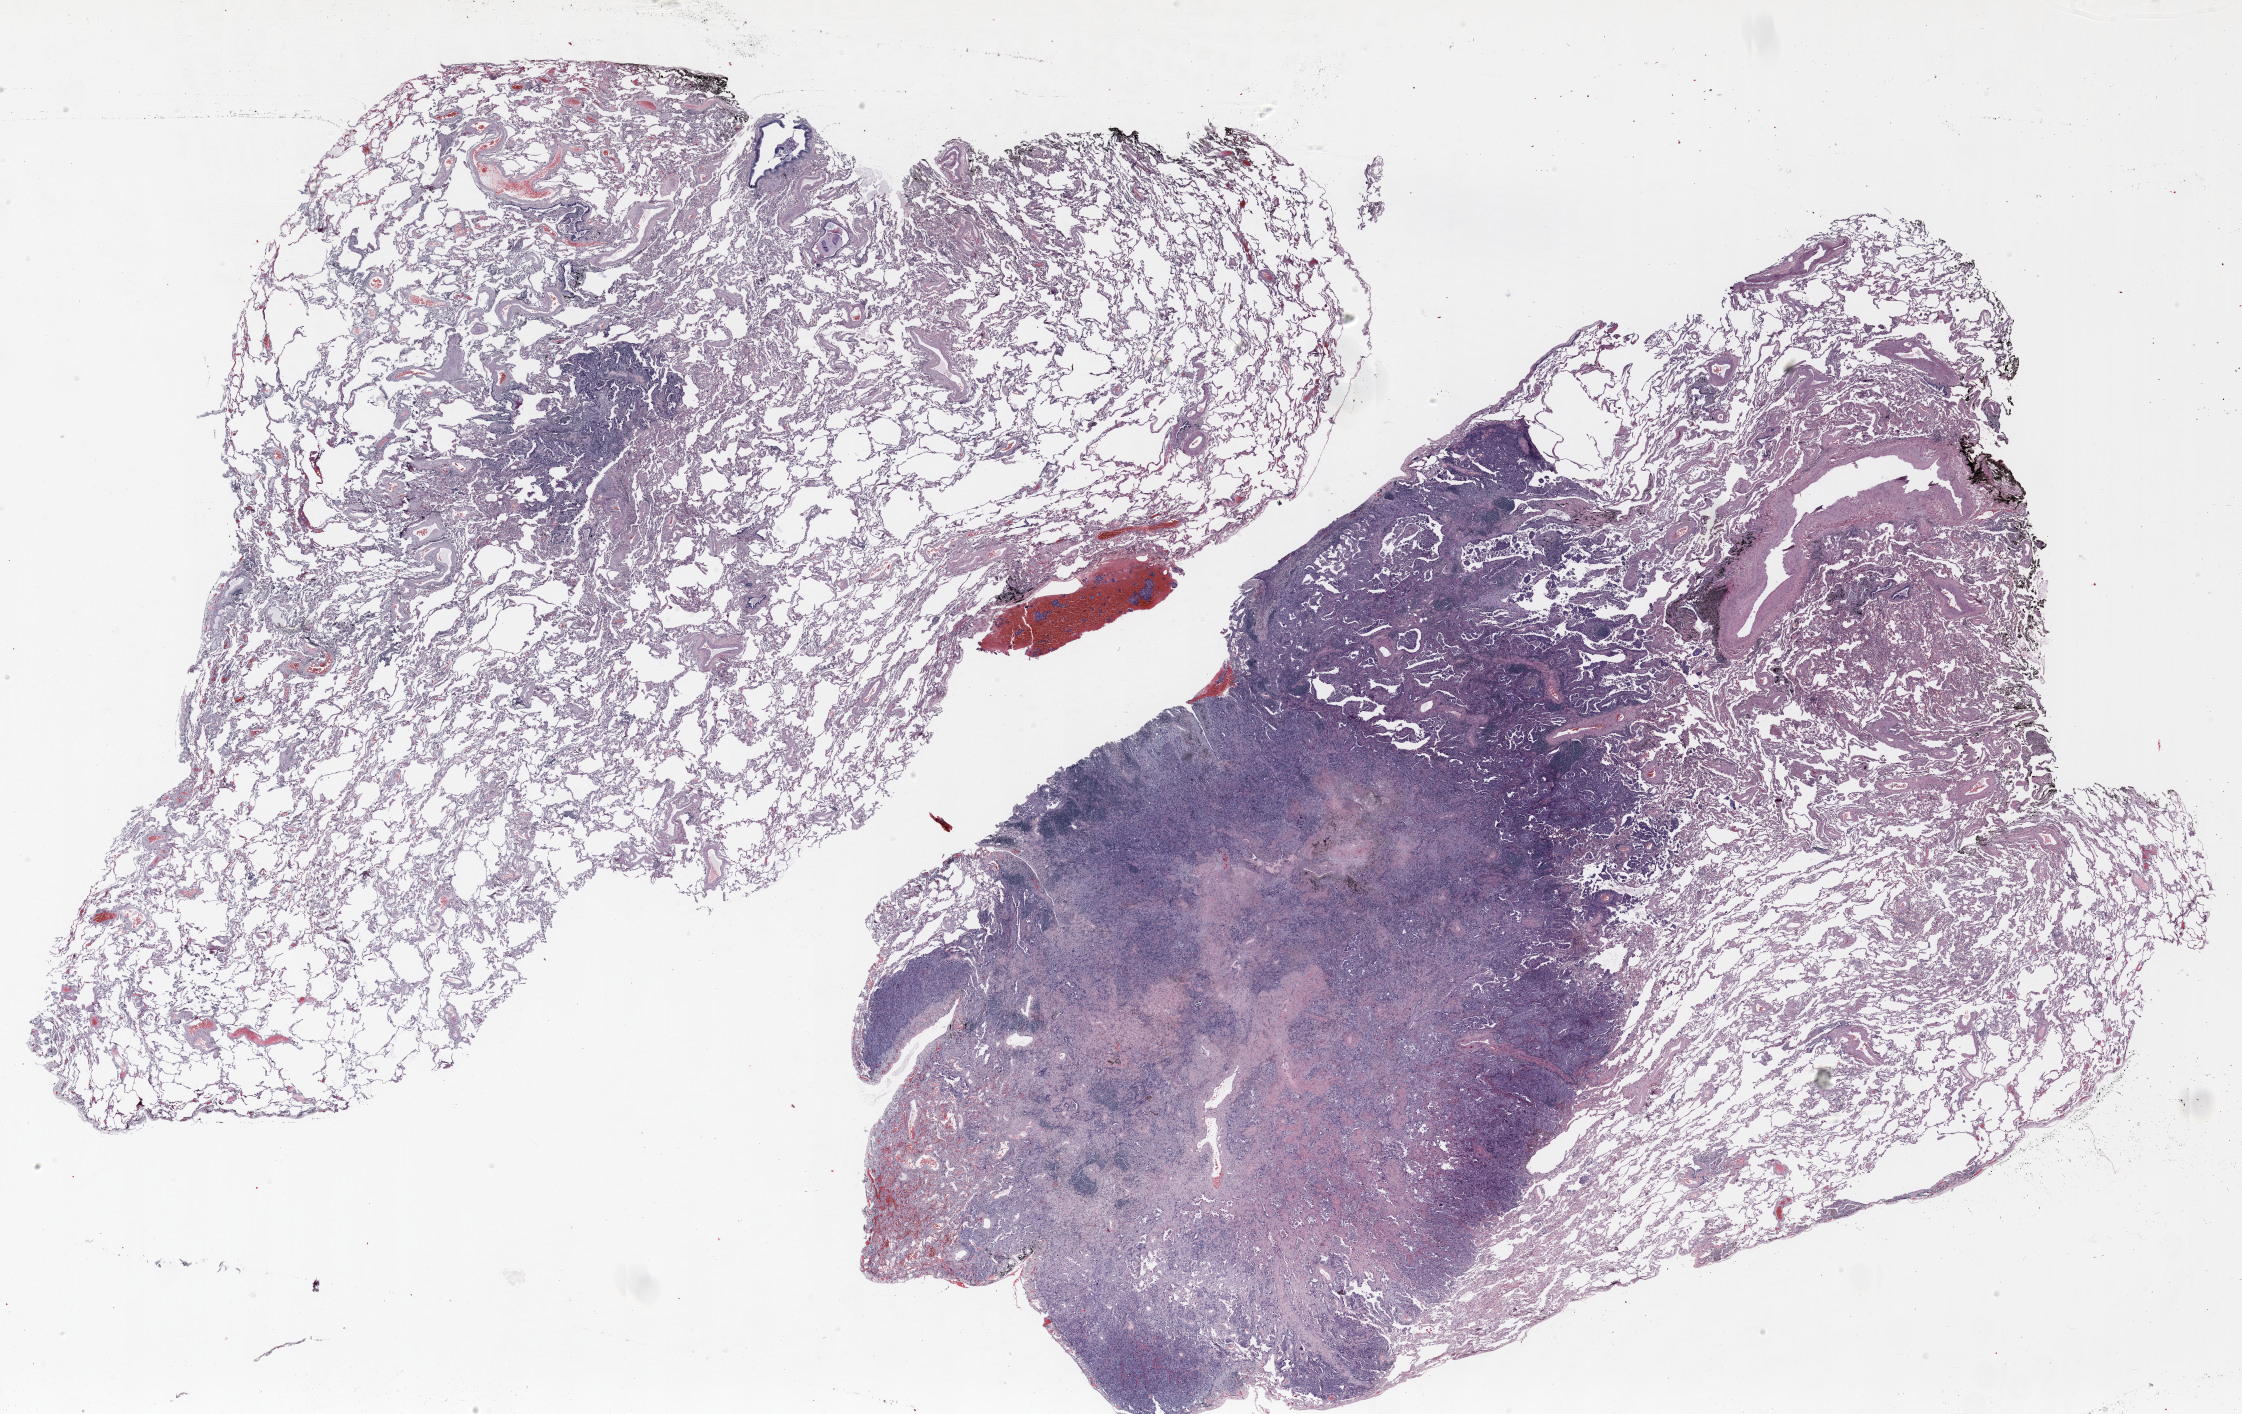
Whole-slide histology image, Hematoxylin and eosin (H&E) stained — low-resolution overview of the scanned area, about 36.0 x 22.7 mm; formalin-fixed paraffin-embedded (FFPE) section; lung tissue. Female patient, aged 74 at enrolment. Current smoker at enrolment. Grade: poorly differentiated (G3).
* participant's lung-cancer diagnosis: Bronchiolo-alveolar adenocarcinoma, NOS
* primary tumour location (clinical record): other location
* tumour size (pathology): 18 mm
* ICD-O-3 topography: lower lobe of lung (C34.3)
* stage (AJCC 6th edition): IV